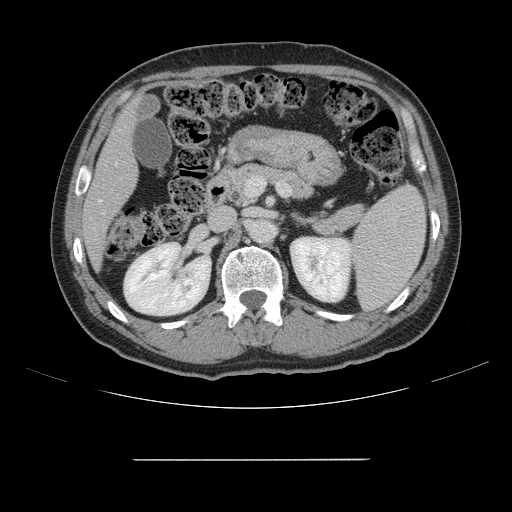
Contrast-enhanced abdominal CT, one axial slice; slice 72 of 164 in the series (ordered by position); 120 kVp; intravenous contrast given; soft-tissue window (W 400 / L 40 HU); 2.5 mm slice thickness; 512 × 512 image matrix. Male patient, age 54 years. Case-level facts recorded for this patient, not image findings: diagnosis: colorectal cancer liver metastases, imaged before liver resection; multiple liver metastases: yes; largest metastasis: 1 cm; disease in both lobes: no.
Annotated regions visible in this slice (expert manual segmentation):
- hepatic veins: box from (x=98, y=163) to (x=117, y=203) px
- liver: (x=85, y=105)–(x=137, y=264)
- planned liver remnant (the part of the liver to remain after resection): (x=85, y=106)–(x=137, y=264)
- portal vein (with intrahepatic branches): (x=102, y=212)–(x=104, y=214)